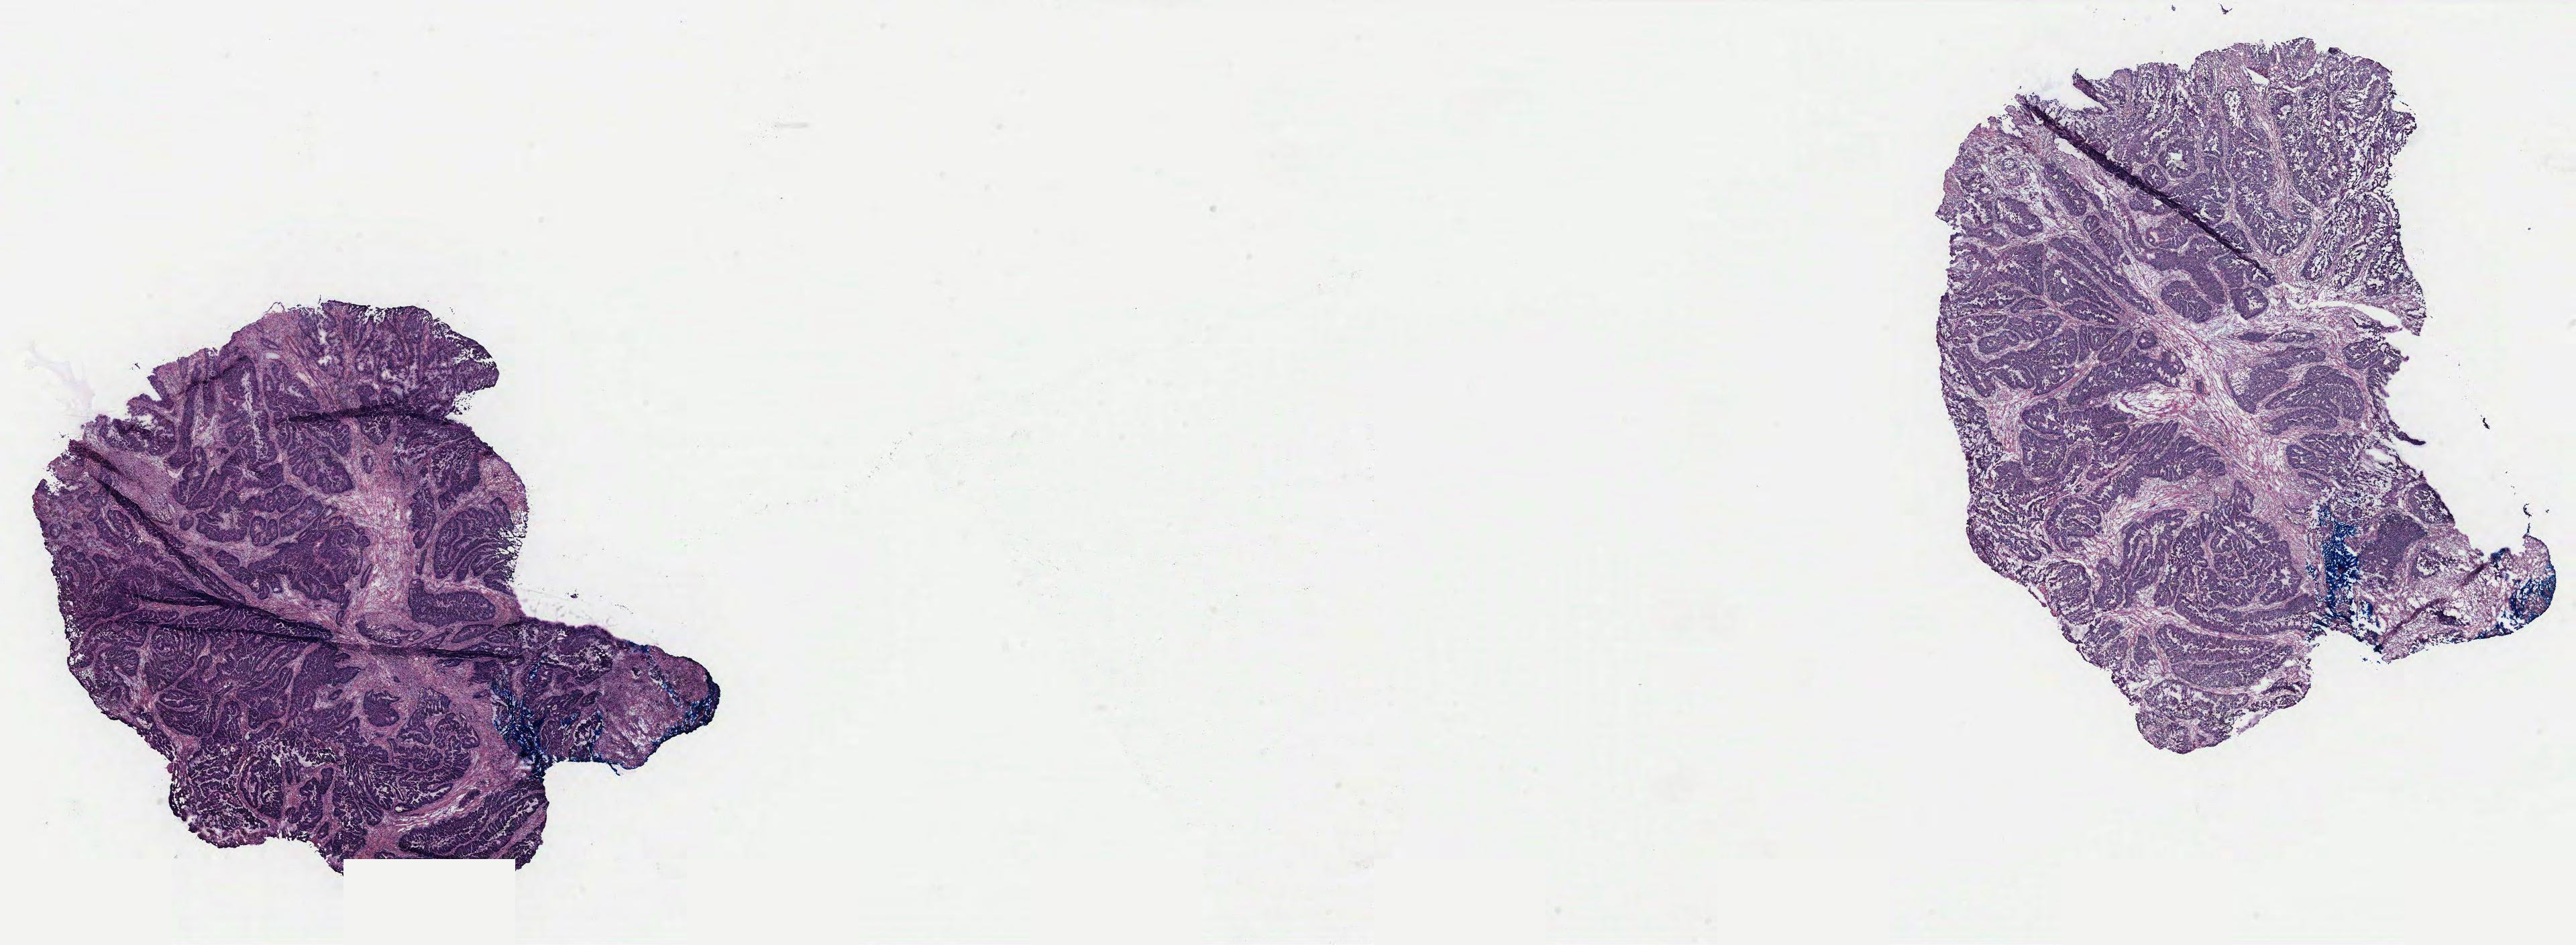
H&E-stained whole-slide image — low-resolution overview of the scanned area, about 30.7 x 11.3 mm (from a 40x scan). Colon, tissue type not recorded. Female patient.
* patient diagnosis: Adenocarcinoma, NOS (rectum, NOS)